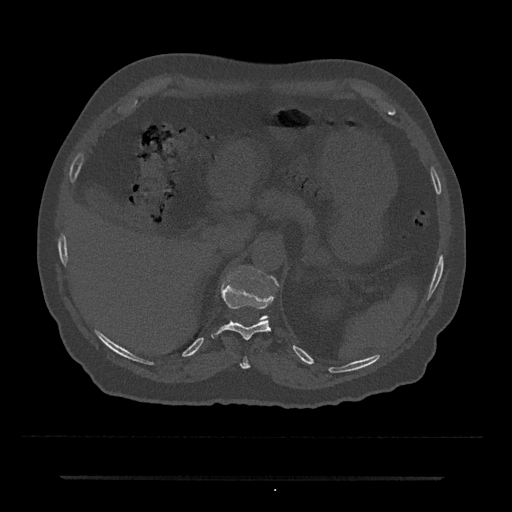
CT including the spine, one axial slice; reconstruction kernel Br40s/3; 120 kVp; bone window (W 1800 / L 400 HU); 0.5 mm slice thickness; 512 × 512 image matrix, field of view 437 × 437 mm. Male patient, age 69 years. Case-level facts recorded for this patient, not image findings: primary cancer: prostate.
Annotated regions visible in this slice (semi-automatic segmentation, software-assisted and operator-edited):
- T10 vertebra: bounding box <240,357,250,369> (left, top, right, bottom; pixels)
- T11 vertebra: <211,285,274,340>
- T12 vertebra: <262,276,278,319>